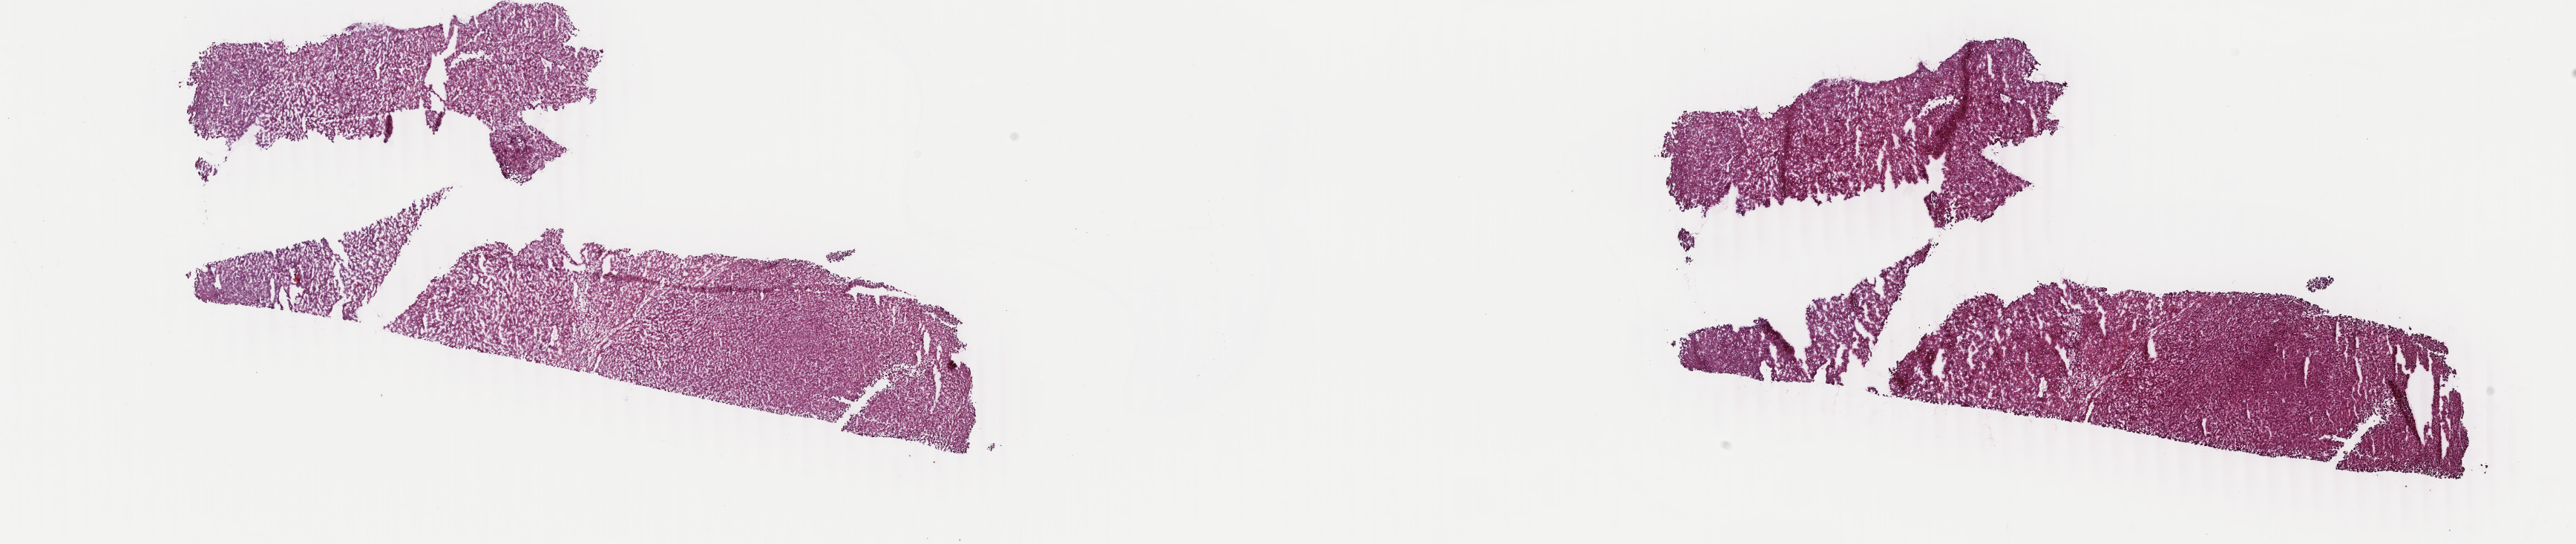
Digitized H&E tissue section (whole slide), whole scanned area (about 27.6 x 5.8 mm, acquisition: 40x scan) shown as a low-resolution overview, frozen section from the top of the tissue portion, primary tumour sample from the liver. Male patient; age at initial diagnosis 58 years. Histologic grade: G1 (well differentiated). Pathologist review of this section (percent, as recorded): tumour cells 80%, tumour nuclei 90%, normal cells 0%, stromal cells 10%, necrosis 10%. Infiltration values recorded for this section: lymphocyte infiltration 0%, monocyte infiltration 0%, neutrophil infiltration 0%.
AJCC pathologic stage: I (7th edition). Pathologic diagnosis: Hepatocellular carcinoma, NOS.